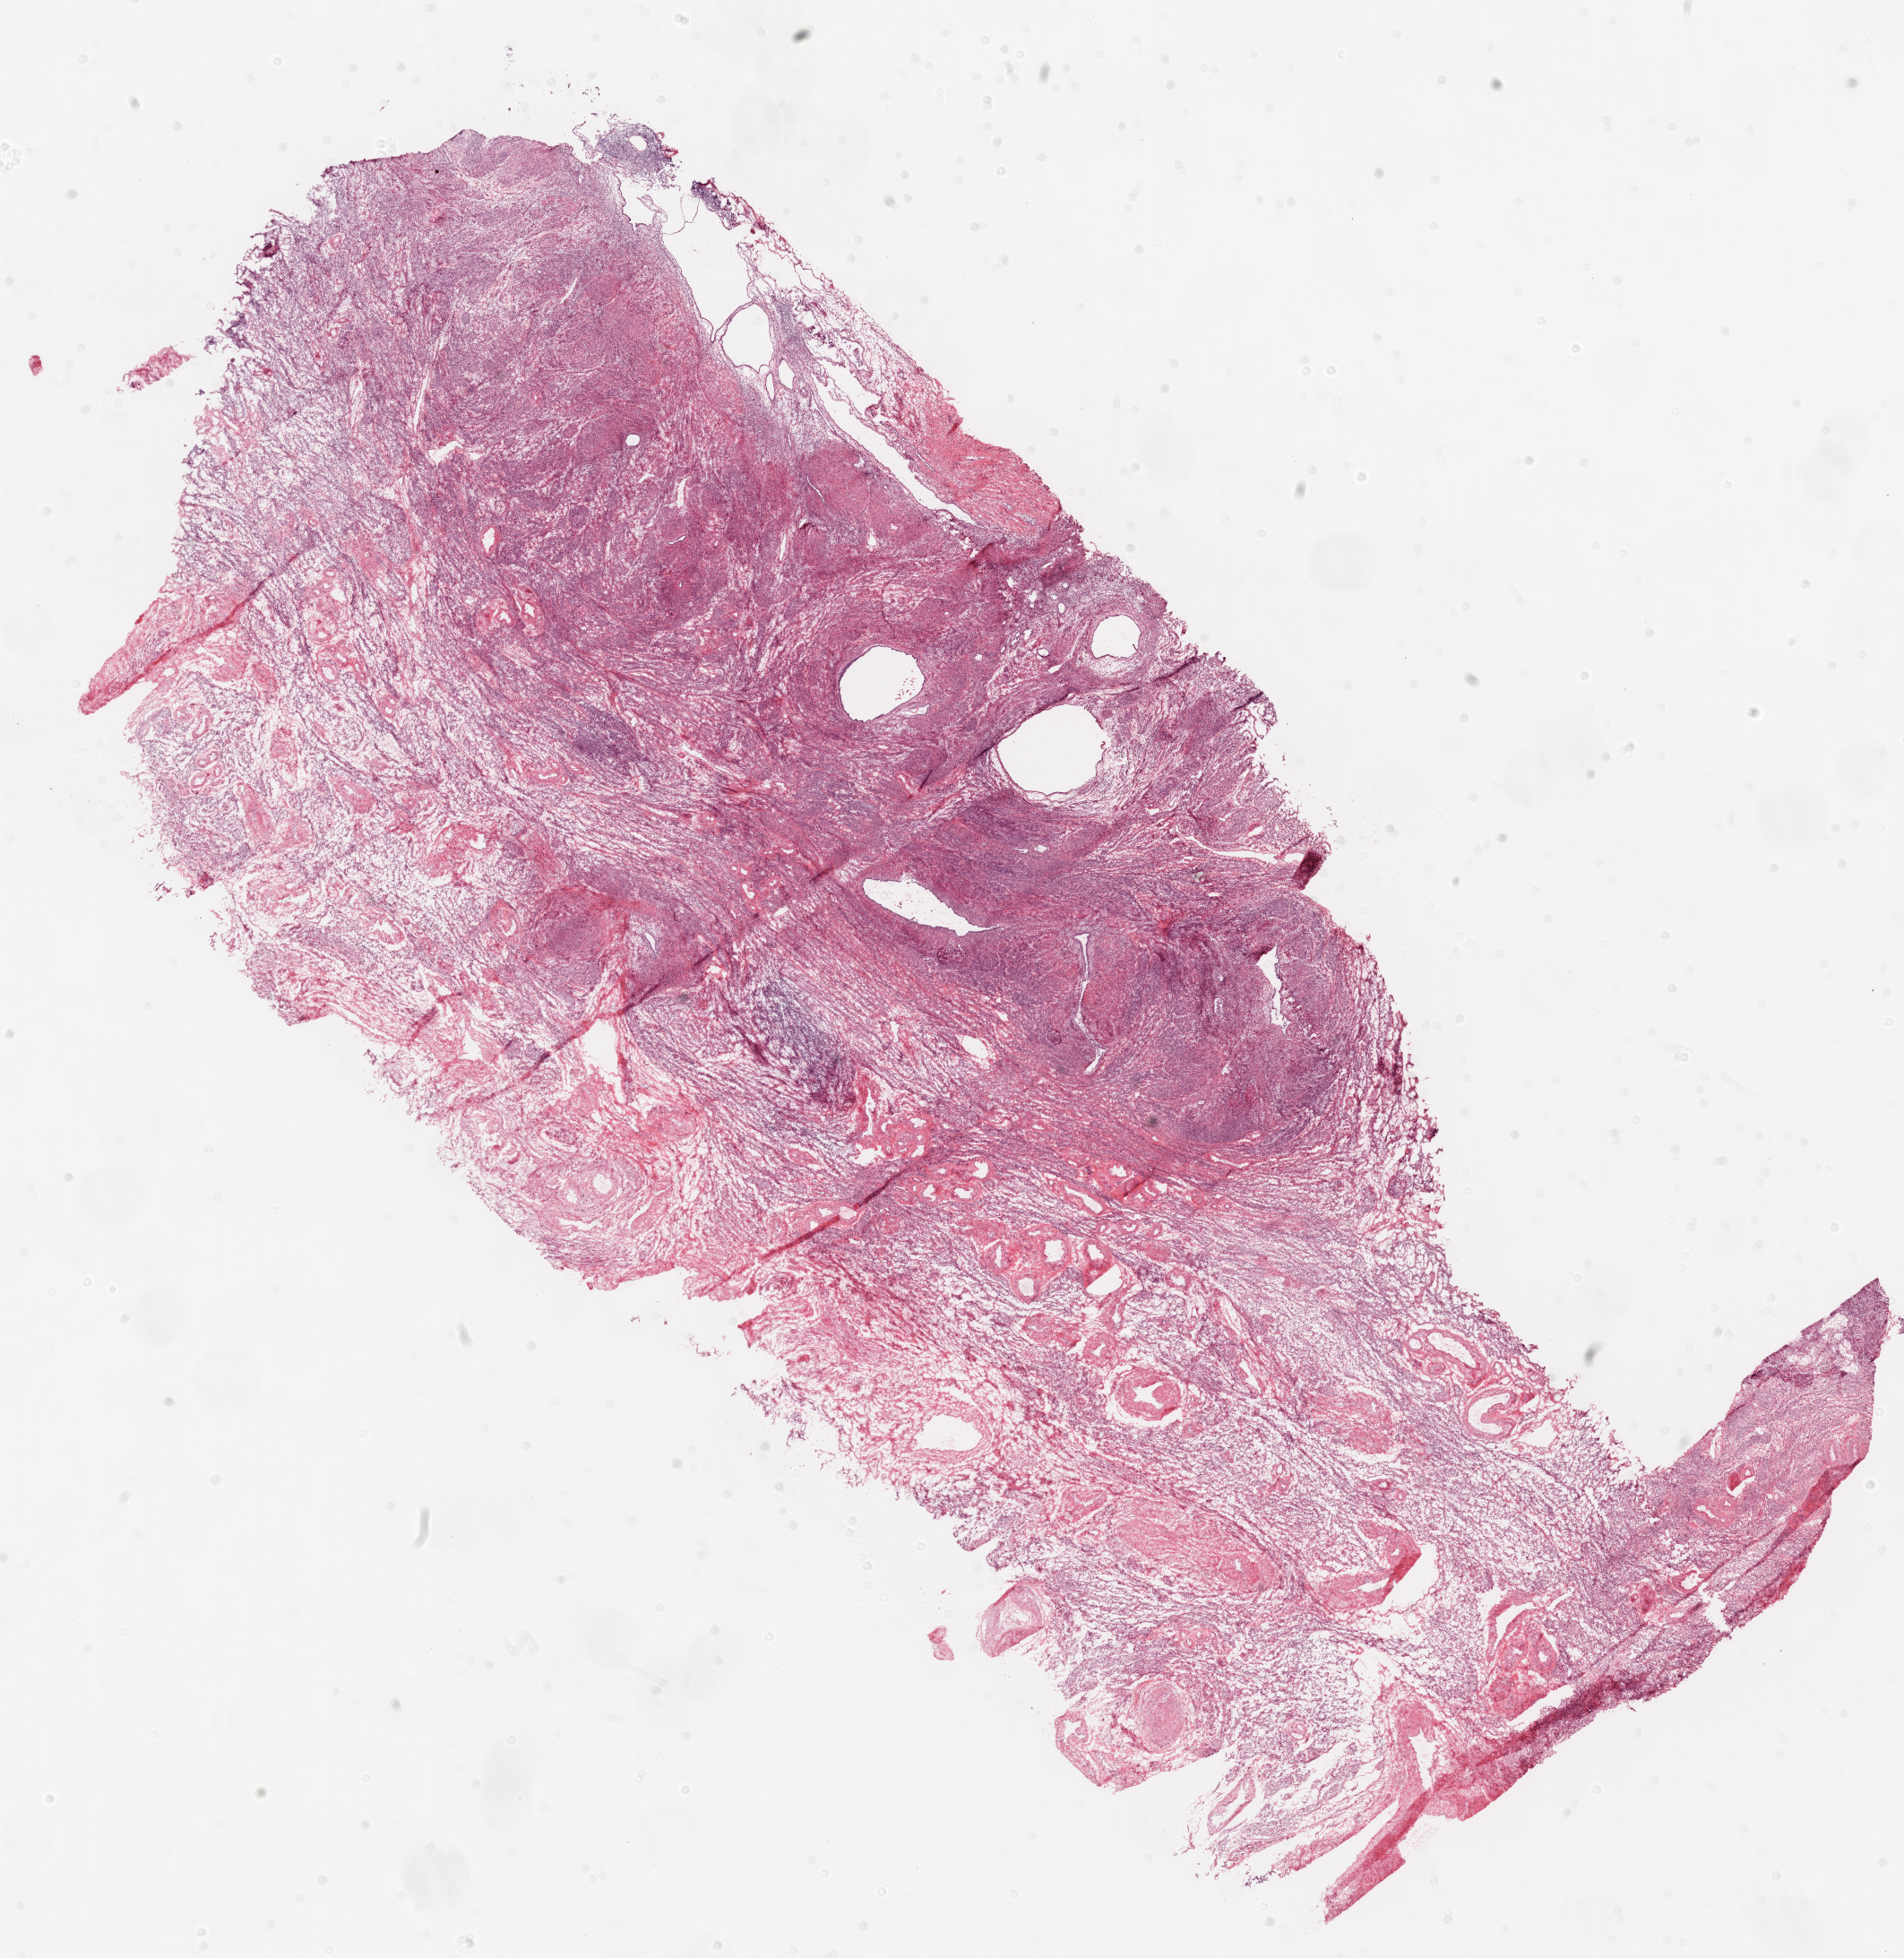
H&E-stained whole-slide image — low-resolution overview of the scanned area, about 17.1 x 17.5 mm (from a 20x scan); frozen section; ovary, solid tissue normal (non-tumour tissue) sample. Female patient; age at initial diagnosis 62 years.
This section: solid tissue normal (non-tumour) sample from the same patient. Patient diagnosis: Serous cystadenocarcinoma, NOS.